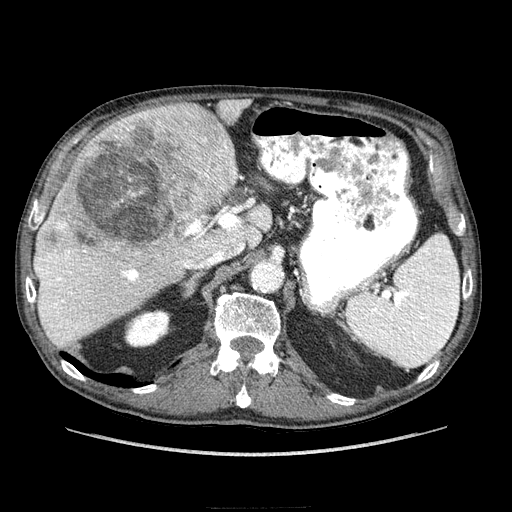
Contrast-enhanced abdominal CT (liver protocol), one axial slice; position 151 of 218 along the scan axis; reconstruction kernel STANDARD; 100 kVp; soft-tissue window (W 400 / L 40 HU); 2.5 mm slice thickness; 512 × 512 image matrix, field of view 380 × 380 mm. From the clinical record (not read from this slice): diagnosis: hepatocellular carcinoma (patient treated with transarterial chemoembolisation; whether this scan precedes or follows treatment is not stated here); TNM stage (as recorded): Stage-IIIA; Child-Pugh class: A; tumour size: 20 cm.
Outlined on this slice (semi-automatically segmented with operator editing):
- liver parenchyma outside the tumour (the mass and vessels are separate outlines, so this box may not span the whole liver): box from (x=34, y=100) to (x=272, y=346) px
- mass: (x=36, y=102)–(x=238, y=267)
- liver vessels: (x=35, y=199)–(x=270, y=337)